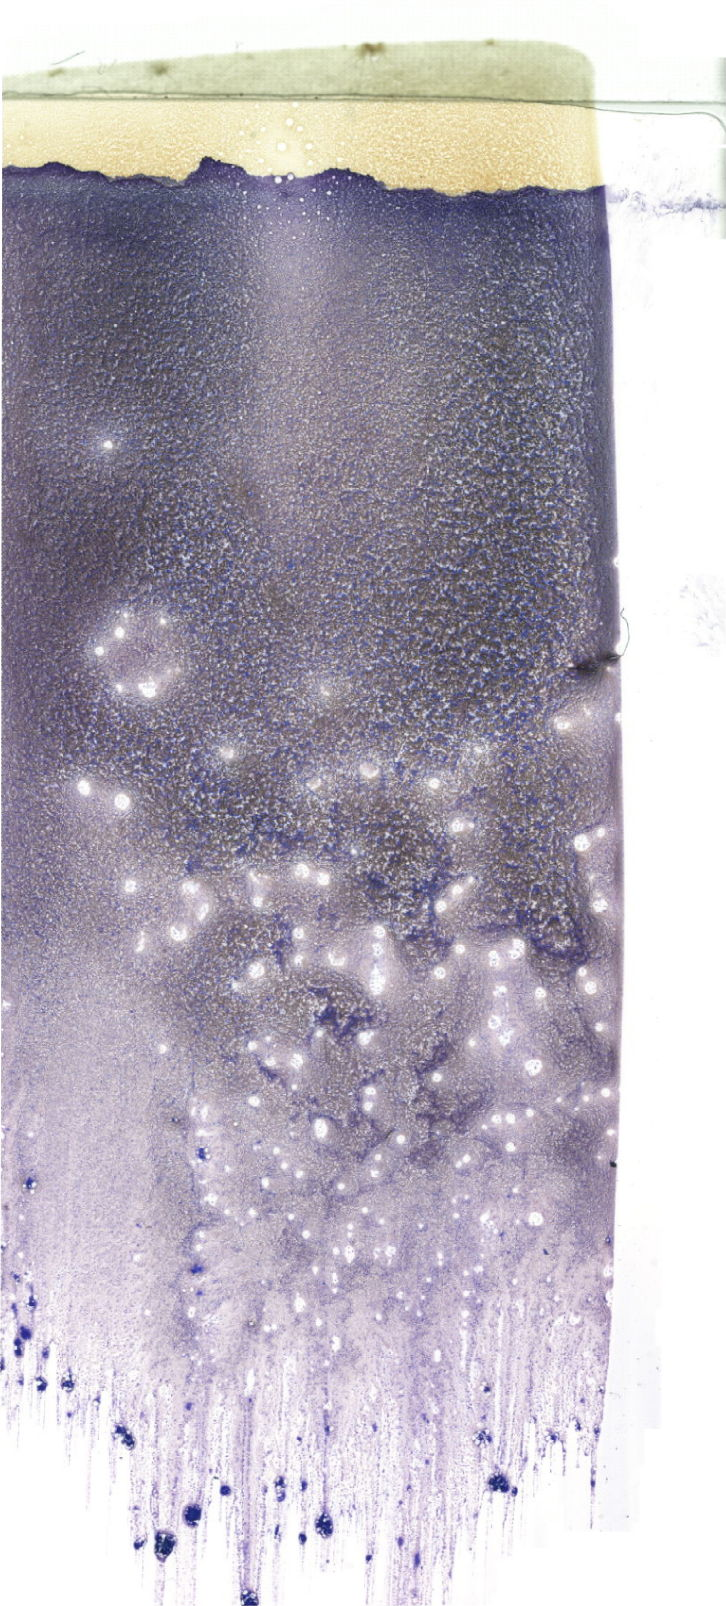
Bone marrow aspirate smear, May-Grünwald–Giemsa stain, whole-slide image — whole scanned area (about 20.6 x 45.5 mm) shown as a low-resolution overview. Patient sex: male.
* diagnosis: Acute Megakaryoblastic Leukemia